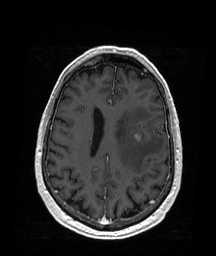
Brain MRI from a brain-tumour surgery series, one axial slice. T1-weighted post-contrast. 1 mm slice thickness. 216 × 256 image matrix, field of view 211 × 250 mm. Case-level facts recorded for this patient, not image findings: histopathology: Metastatic Melanoma; tumour location: Left Frontal.
Annotated regions visible in this slice (manually delineated by an expert):
- tumour: bounding box <135,135,143,141> (left, top, right, bottom; pixels)